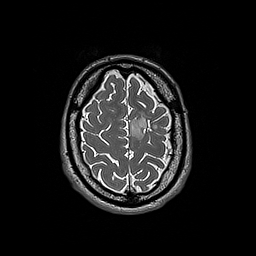
Brain MRI from a brain-tumour surgery series, one axial slice. Slice 47 of 192 in the series (ordered by position). 1 mm slice thickness. 256 × 256 image matrix, field of view 250 × 250 mm. Case-level facts recorded for this patient, not image findings: histopathology: Oligodendroglioma; WHO grade: 3; IDH mutation: yes; tumour location: Left Frontal.
Outlined on this slice (outlined manually by an expert reader):
- tumour: bounding box <130,113,157,140> (left, top, right, bottom; pixels)